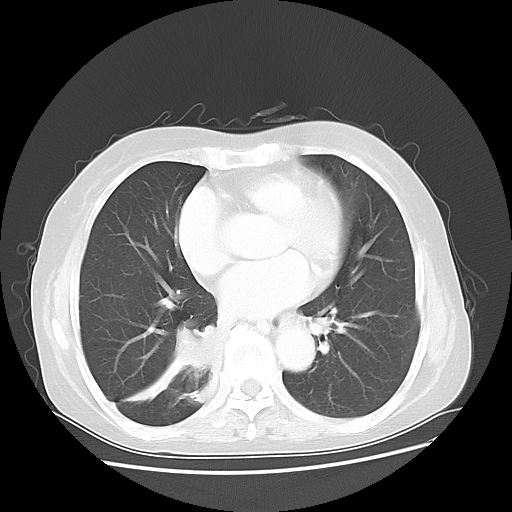
Chest CT, one axial slice; slice 19 of 47 in the series (ordered by position); reconstruction kernel LUNG; lung window (W 1500 / L -600 HU); 5 mm slice thickness; 512 × 512 image matrix, field of view 360 × 360 mm. Female patient, age 63 years. Case-level facts recorded for this patient, not image findings: clinical TNM (as recorded): T2 N3 M1b.
Outlined on this slice (bounding box drawn by a radiologist):
- lung tumour (recorded histology: small cell carcinoma): bounding box <163,321,223,392> (left, top, right, bottom; pixels)